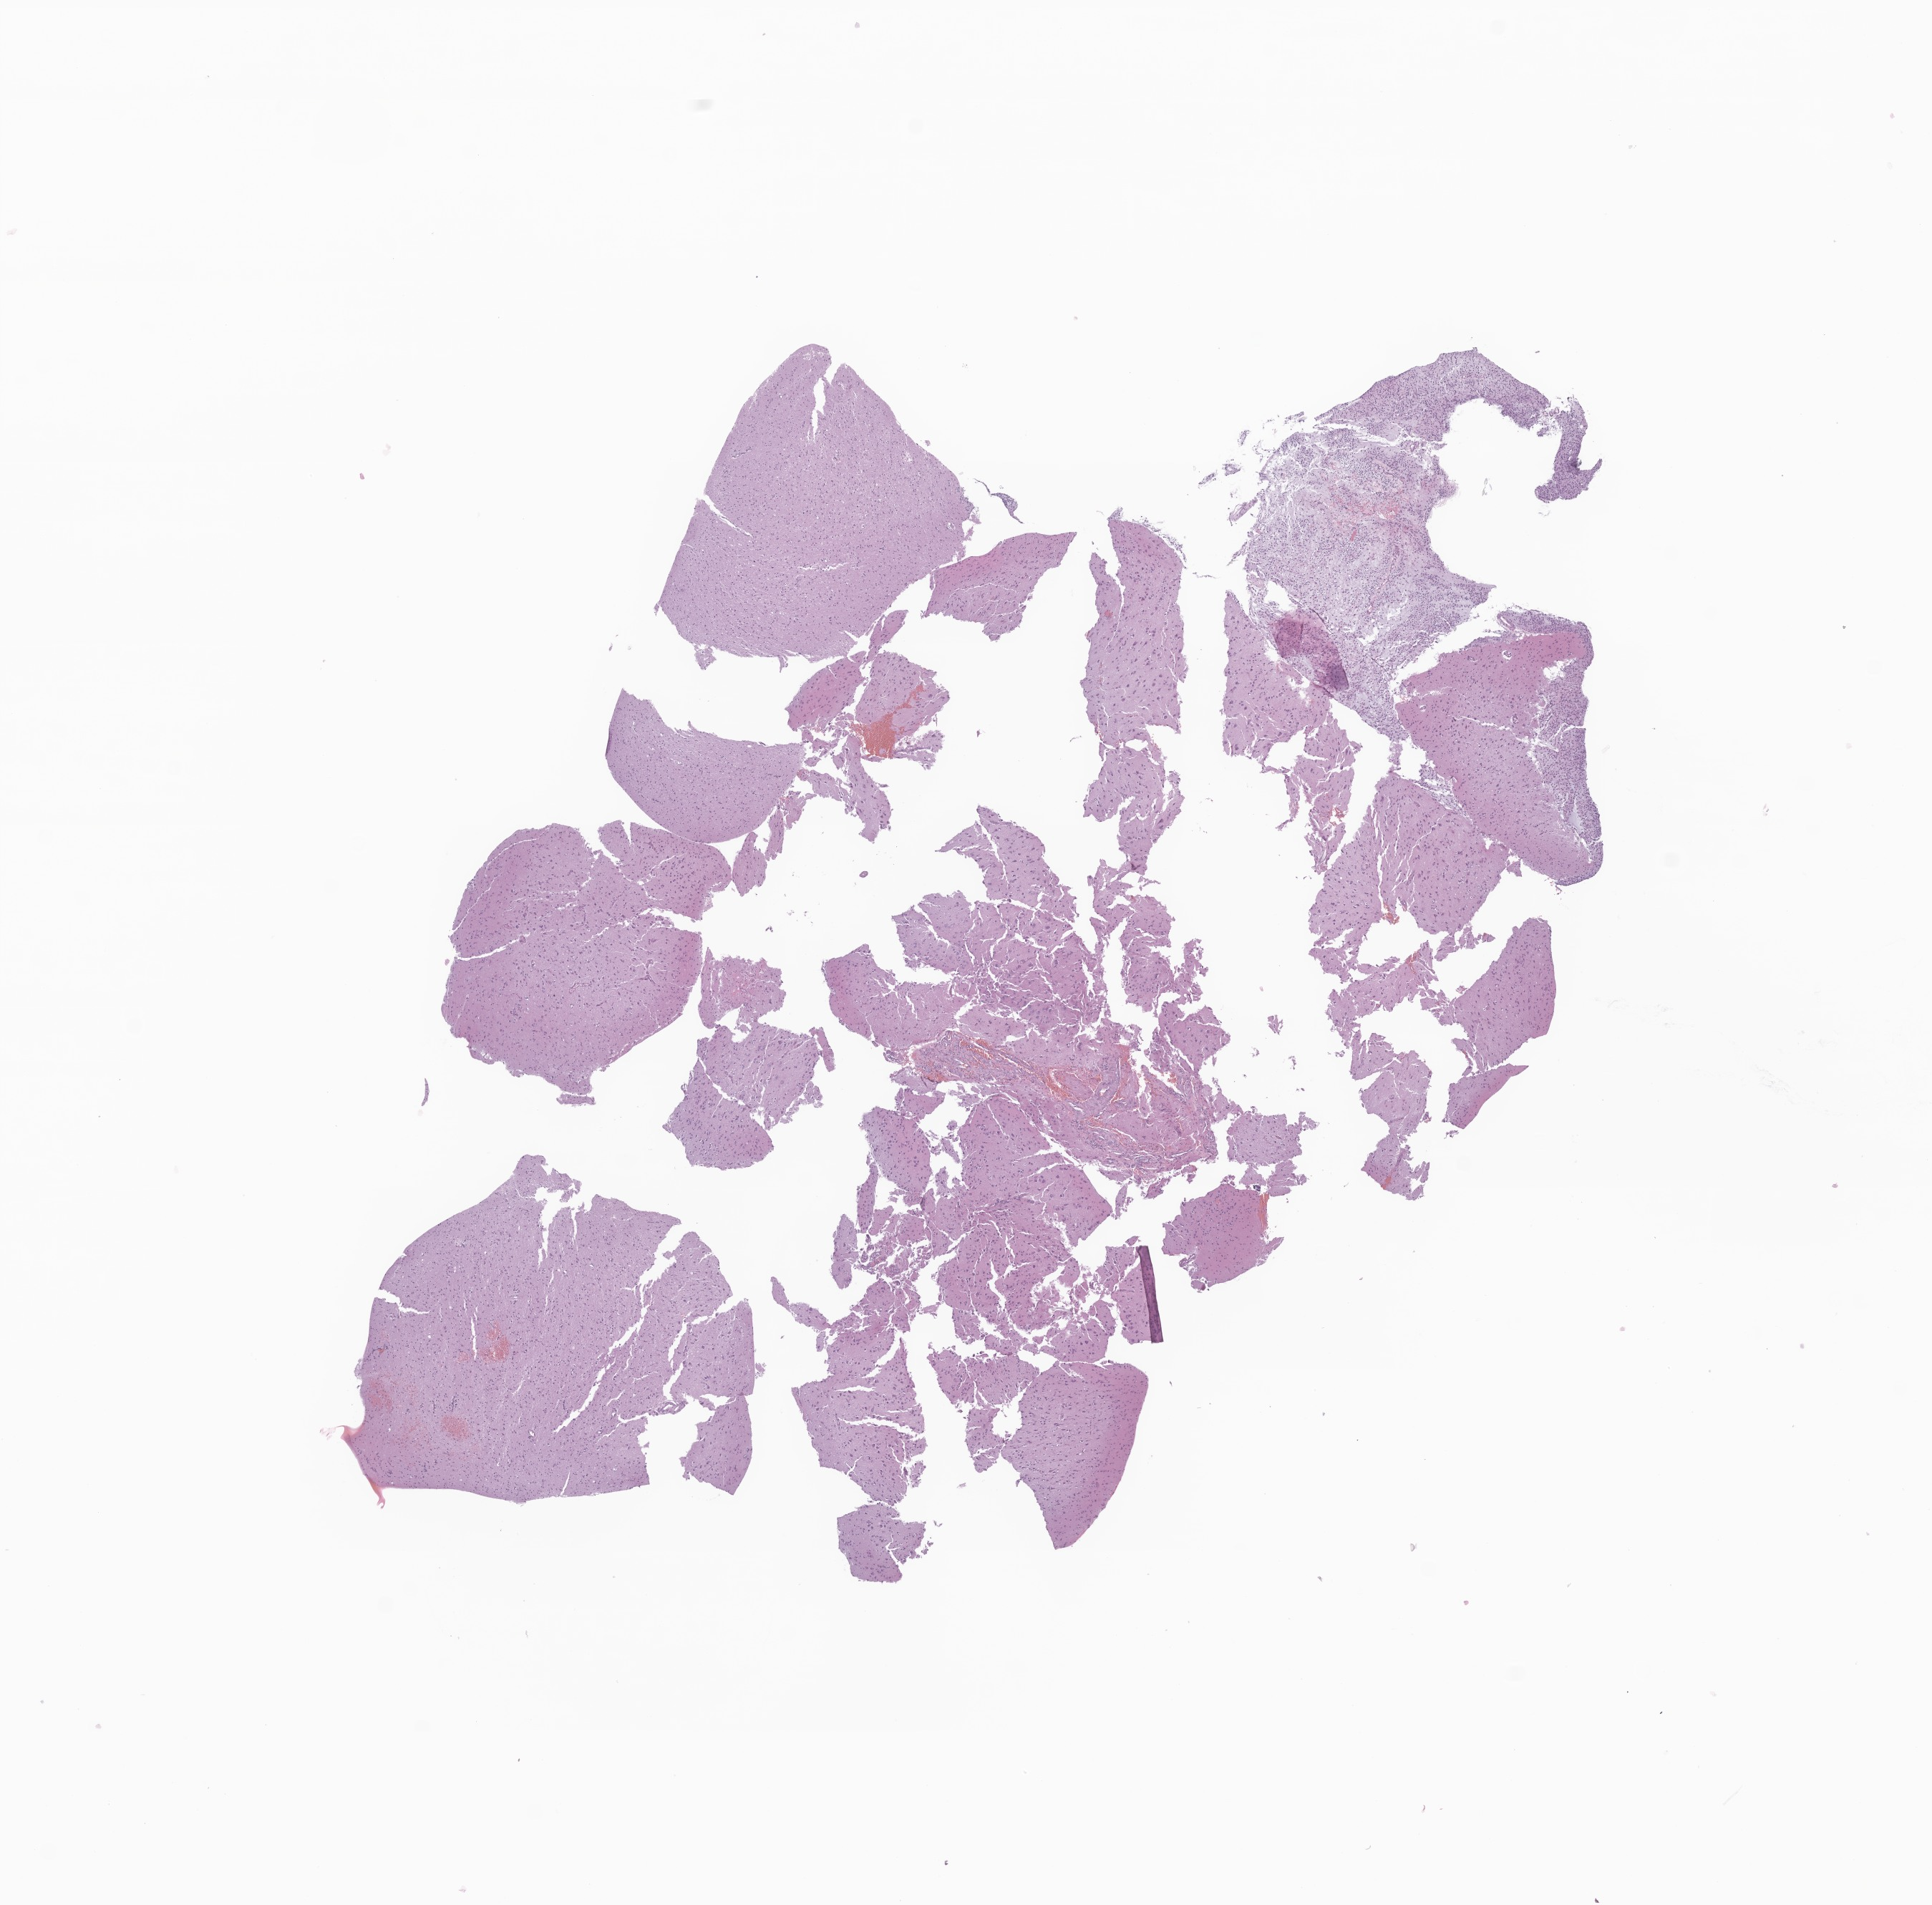
Whole-slide image, hematoxylin and eosin (H&E) stain of tumor tissue from the brain — whole scanned area (about 11.4 x 11.2 mm) shown as a low-resolution overview; formalin-fixed, paraffin-embedded (FFPE) tissue. Male patient, age 219 months (18 years 3 months).
Recorded diagnosis: Dysembryoplastic neuroepithelial tumor.